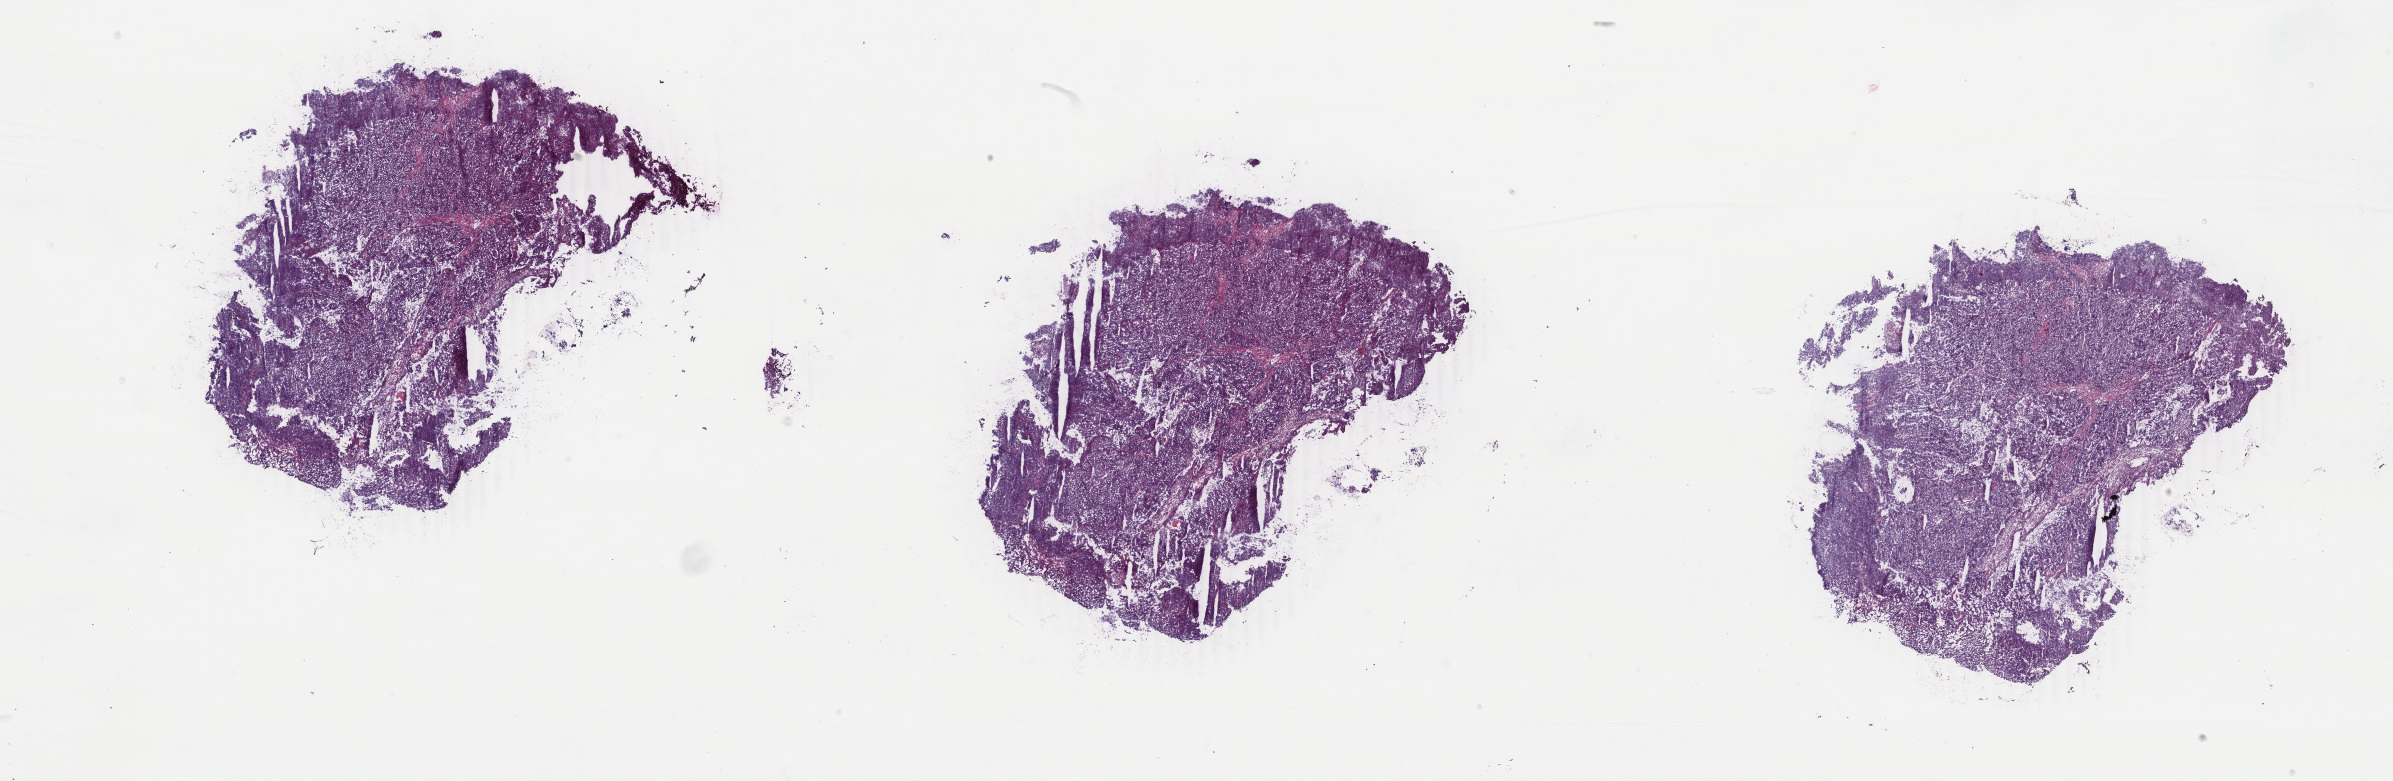
H&E whole-slide image — shown as a low-resolution overview of the whole scanned area (about 38.1 x 12.4 mm, slide scanned at 40x), frozen section, sample: primary tumour, breast. Female, age 61 years at initial diagnosis. Composition of this section per pathologist review: tumour cells 95%, tumour nuclei 95%, normal cells 0%, stromal cells 5%, necrosis 0%. Infiltration values recorded for this section: lymphocyte infiltration 0%, monocyte infiltration 0%, neutrophil infiltration 0%.
AJCC pathologic stage: IIA. Histologic diagnosis: Infiltrating duct carcinoma, NOS. Laterality: left.